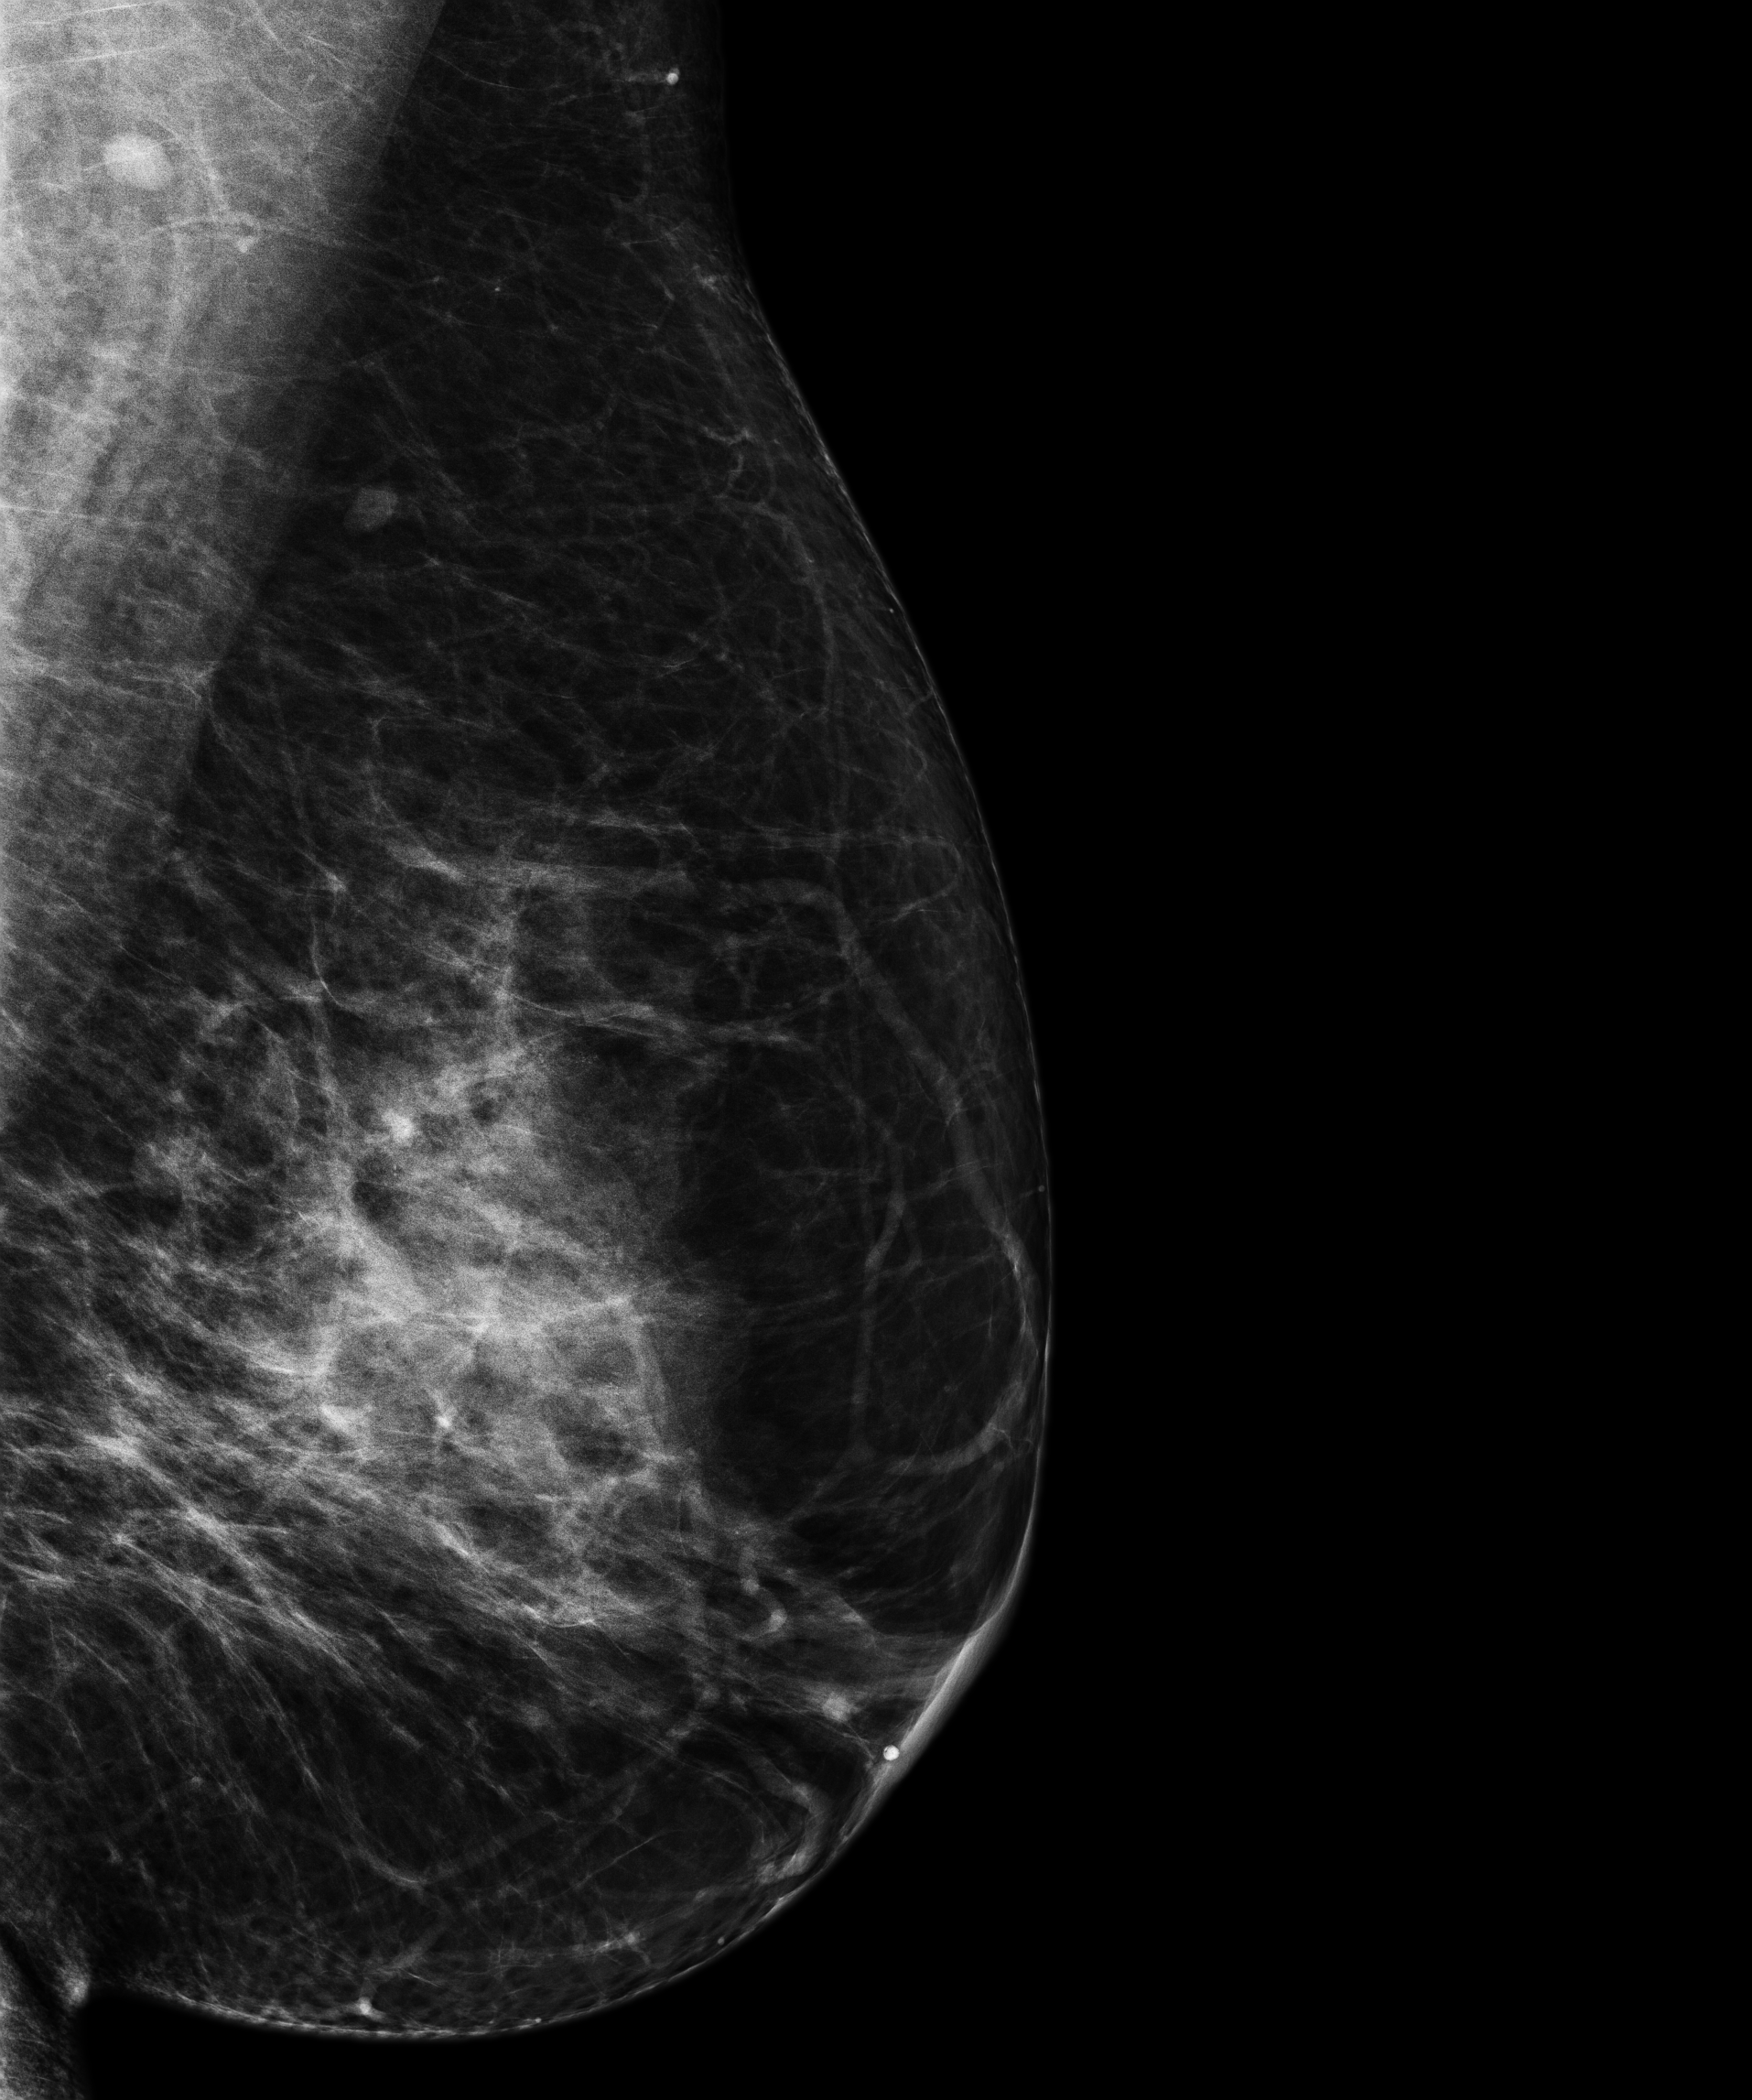
Screening examination, compressed breast thickness 83.5 mm. Patient: female, 48 years.
Image type: full-field digital mammogram. Breast: left. Projection: mediolateral oblique (MLO) view.